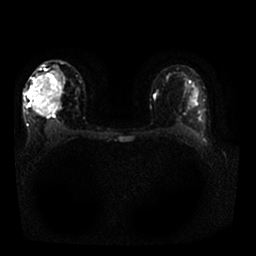
Breast MRI, one axial slice. Slice 11 of 25 in the series (ordered by position). Diffusion-weighted series; image 2 of 4 stored at this slice position (different b-values; order by instance number). 1.5 T. 256 × 256 image matrix, field of view 340 × 340 mm. Female patient.
Annotated regions visible in this slice (outlined manually by an expert reader):
- tumour on diffusion-weighted imaging: bounding box <26,90,32,96> (left, top, right, bottom; pixels)